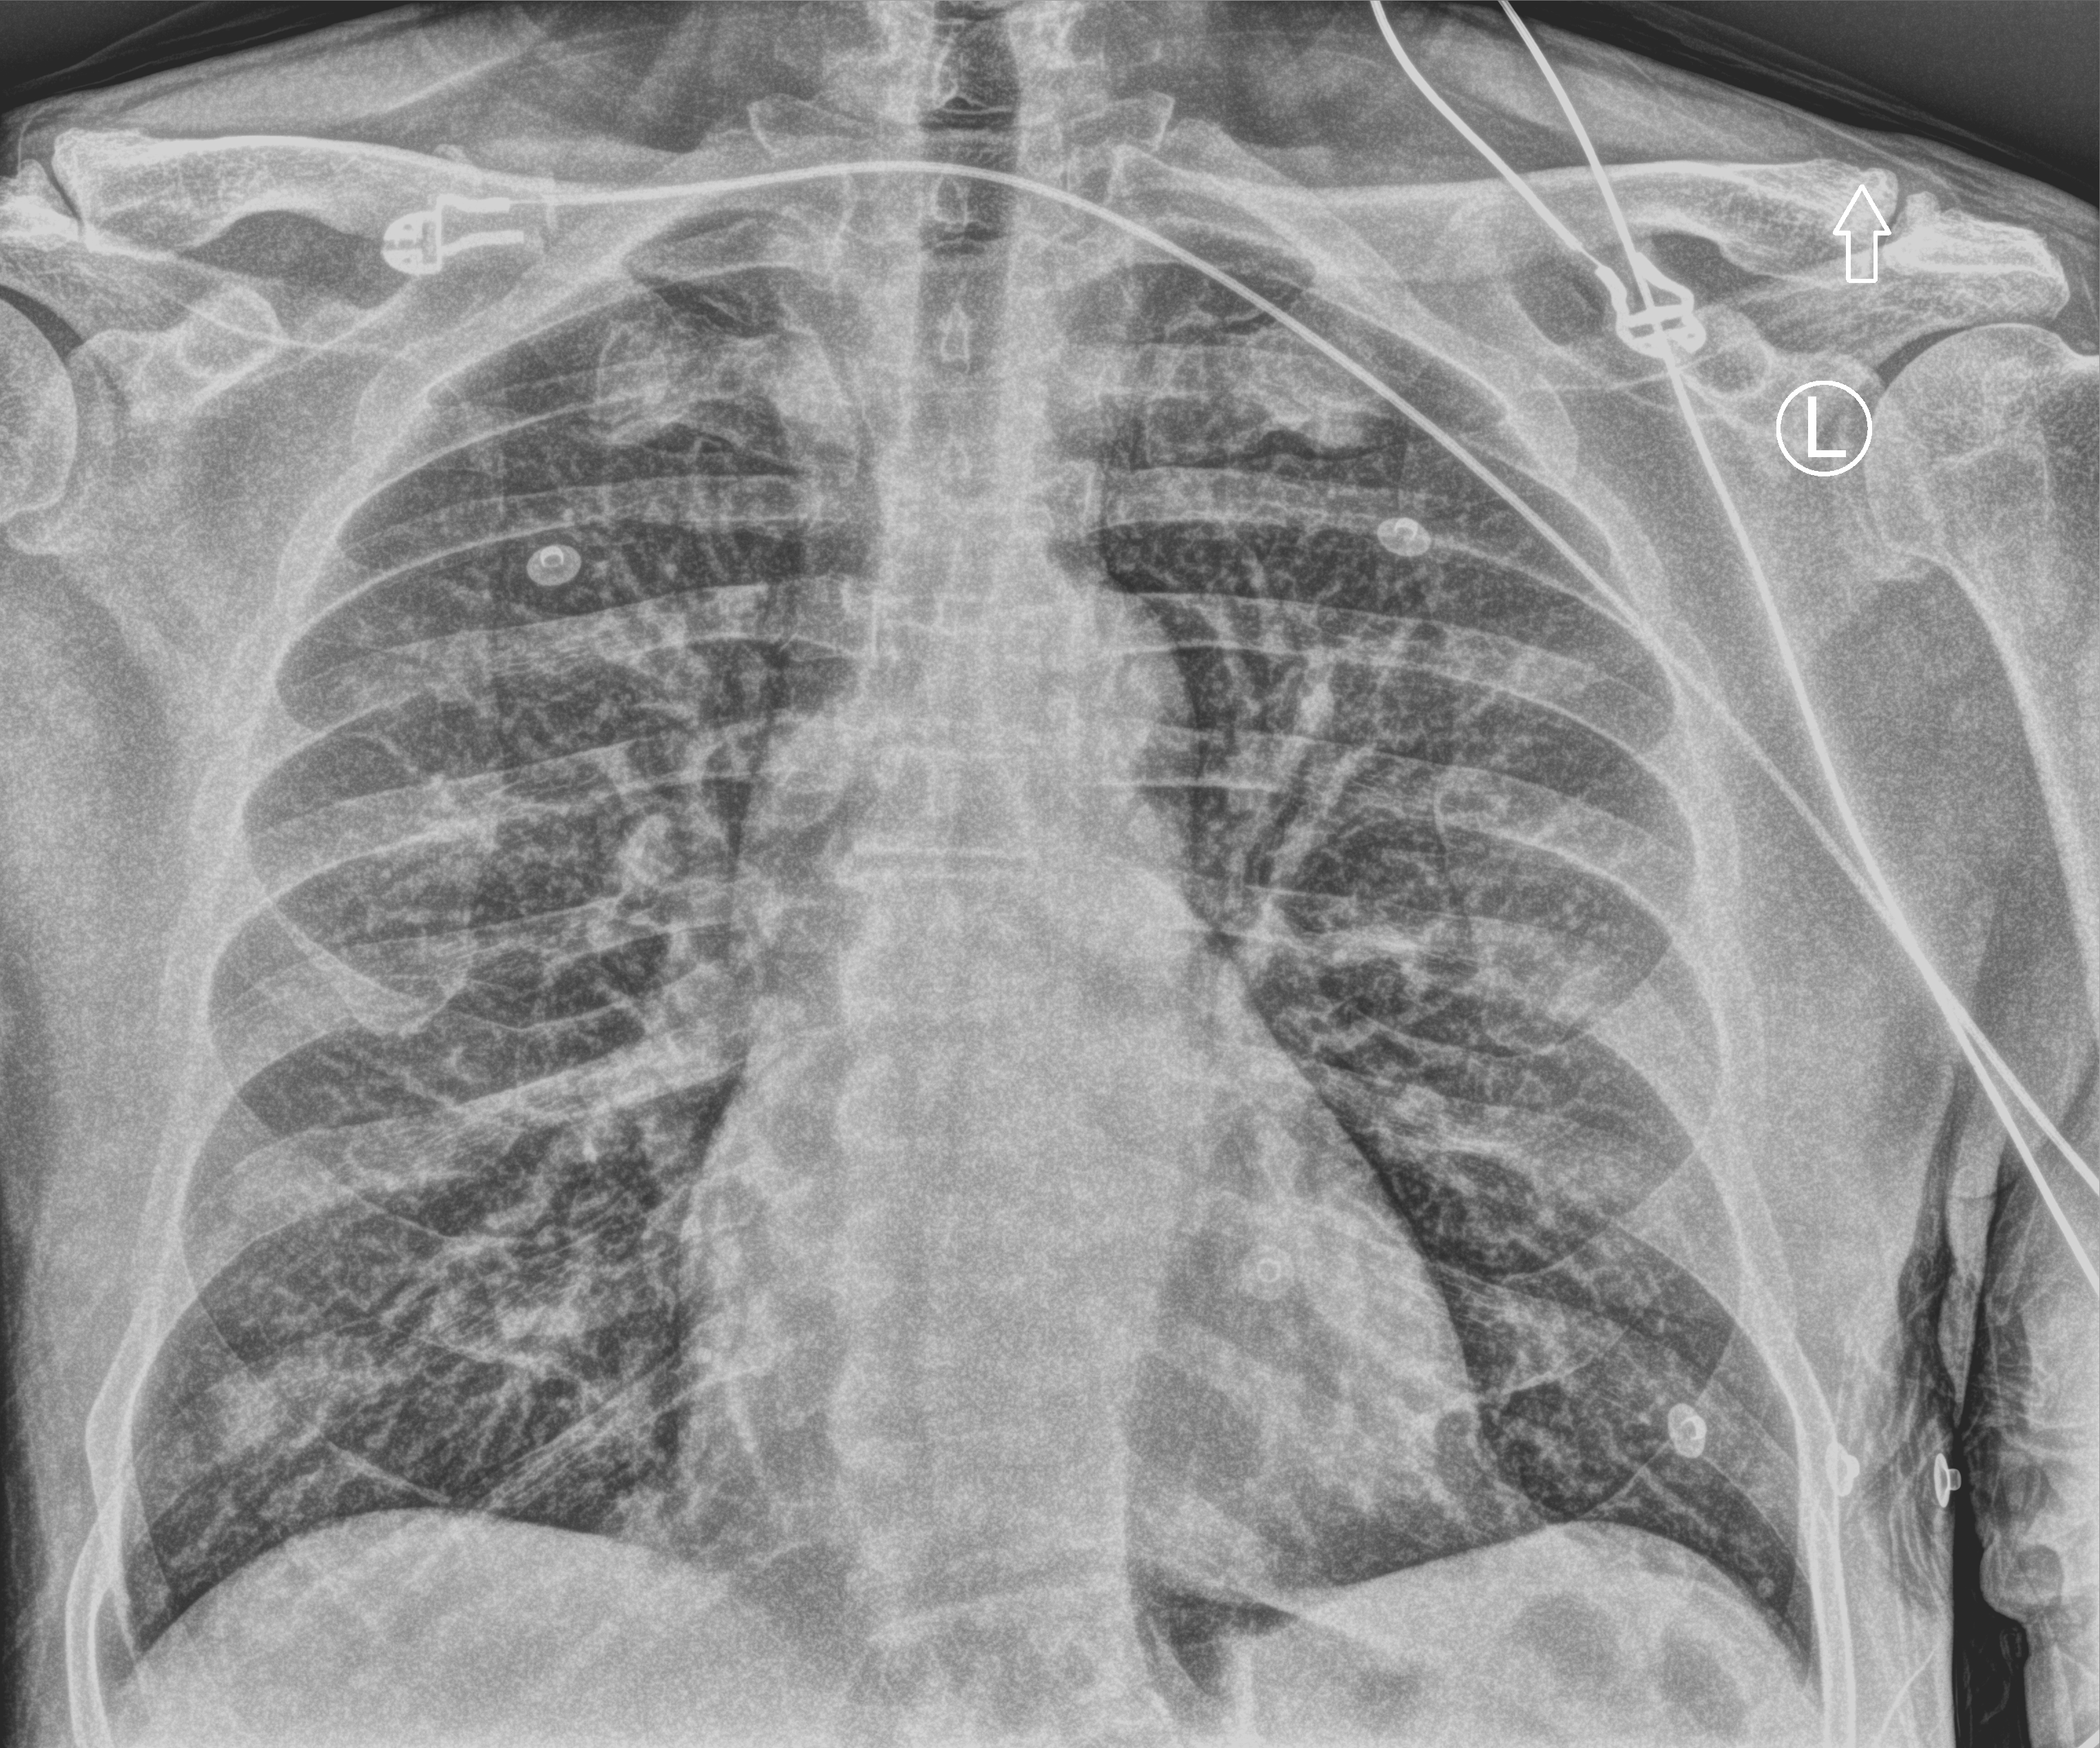
Bedside chest radiograph (computed radiography). Male patient hospitalised with COVID-19, age 18–59 years.
From the hospital-stay record, not from the radiograph (when in the stay this image was taken is not recorded): mechanically ventilated during this hospital stay: no.